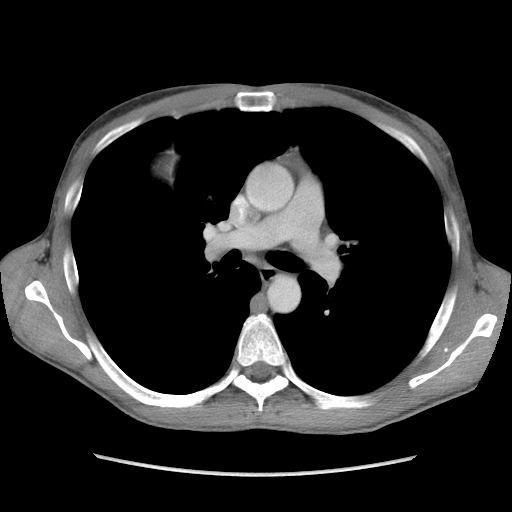
Contrast-enhanced abdominal CT, one axial slice. Slice 108 of 115 in the series (ordered by position). Soft-tissue window (W 400 / L 40 HU). 5 mm slice thickness. 512 × 512 image matrix, field of view 360 × 360 mm. Male patient. Case-level facts recorded for this patient, not image findings: diagnosis: adrenocortical carcinoma; tumour side: right adrenal; Ki-67 index: 13 %; stage (as recorded): 3.
Structures marked on this image (semi-automatic segmentation, software-assisted and operator-edited):
- mass: bounding box (x1, y1, x2, y2) in pixels: (155, 157, 173, 175)